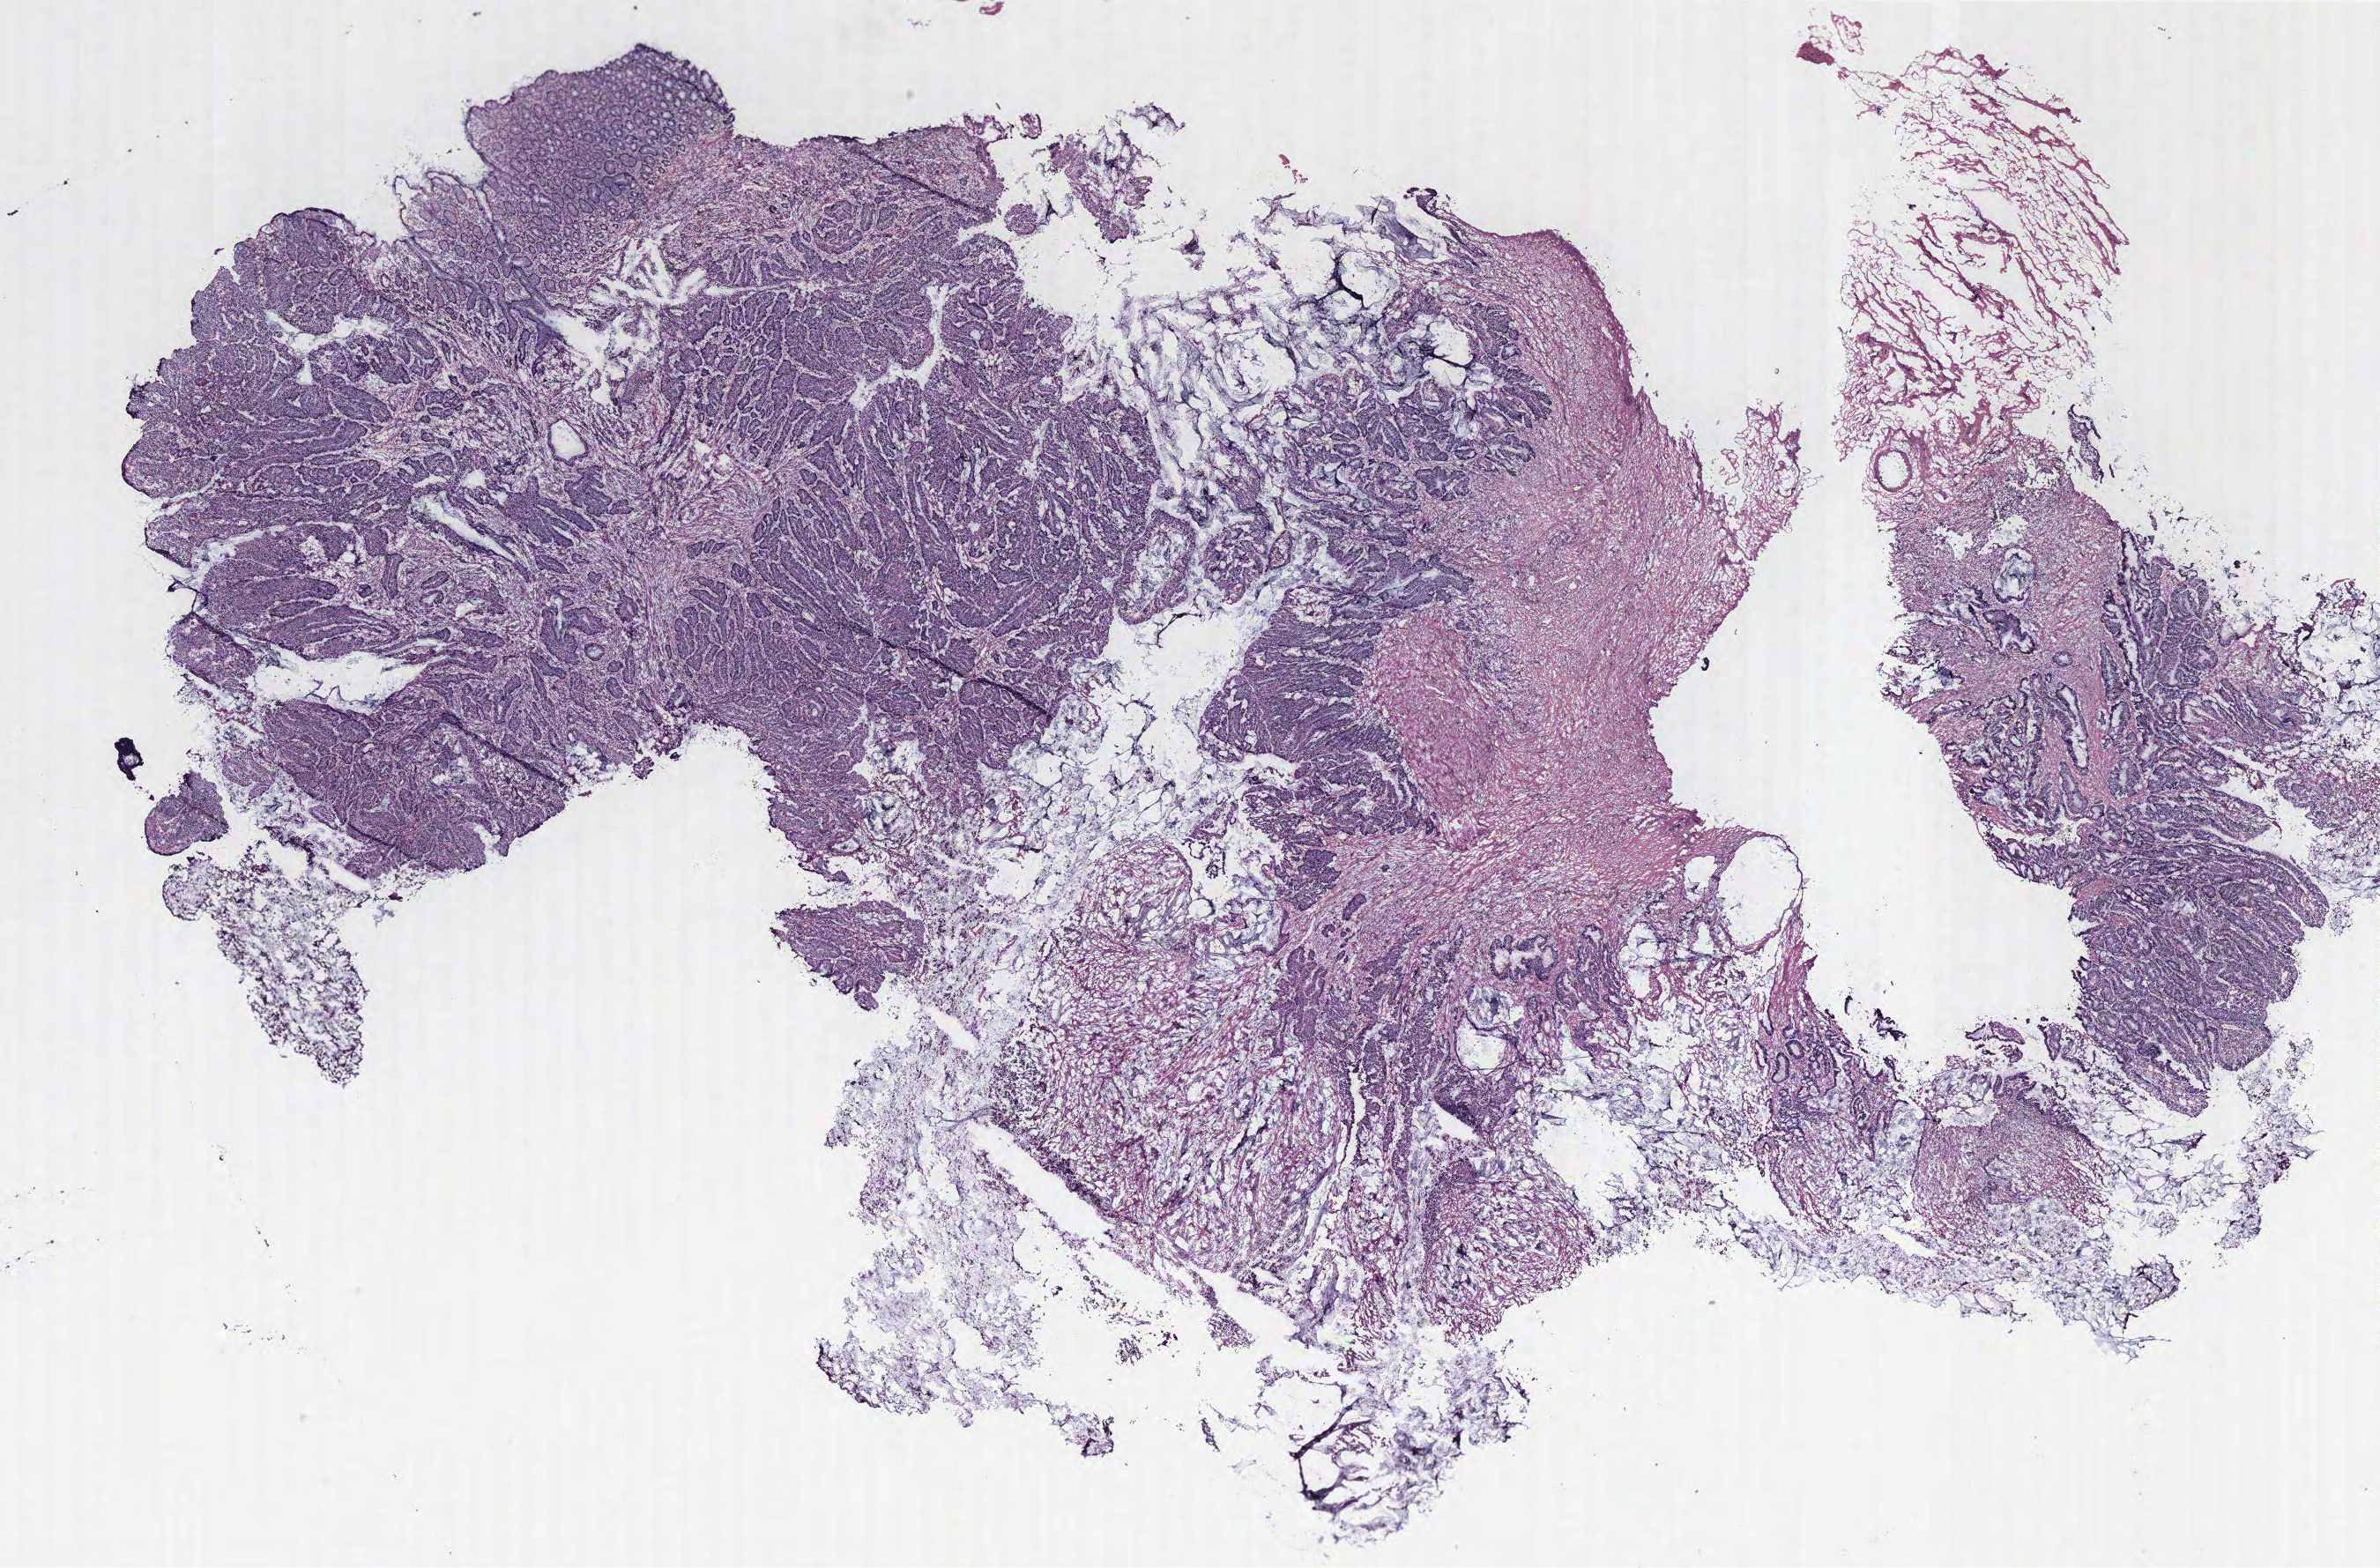
H&E whole-slide image — whole scanned area (about 21.6 x 14.2 mm, slide scanned at 40x) shown as a low-resolution overview, tumour tissue sample, colon. 74-year-old male patient.
- diagnosis: Adenocarcinoma, NOS
- AJCC pathologic stage: IVA
- primary tumour site (as recorded): colon